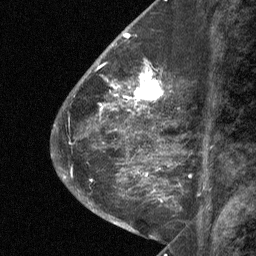
Breast MRI (dynamic contrast-enhanced), one sagittal slice; slice 24 of 64 in the series (ordered by position); dynamic contrast-enhanced study with each time point stored as its own series, time point 2 of 3 at this slice position (early post-contrast, ordered by acquisition time); 1.5 T; TE 4.8 ms, TR 27 ms; 256 × 256 image matrix, field of view 180 × 180 mm. Female patient, age 59 years. From the clinical record (not read from this slice): setting: breast cancer imaged before/during neoadjuvant chemotherapy; receptor status: triple-negative.
Annotated regions visible in this slice (semi-automatic segmentation, software-assisted and operator-edited):
- analysis volume of interest (the breast-tissue region the enhancement analysis was run in; not a lesion): bounding box [x1, y1, x2, y2] px = [122, 60, 176, 109]
- tumour enhancement mask (voxels above the 90 % enhancement threshold inside the analysis volume of interest): [124, 61, 163, 109]